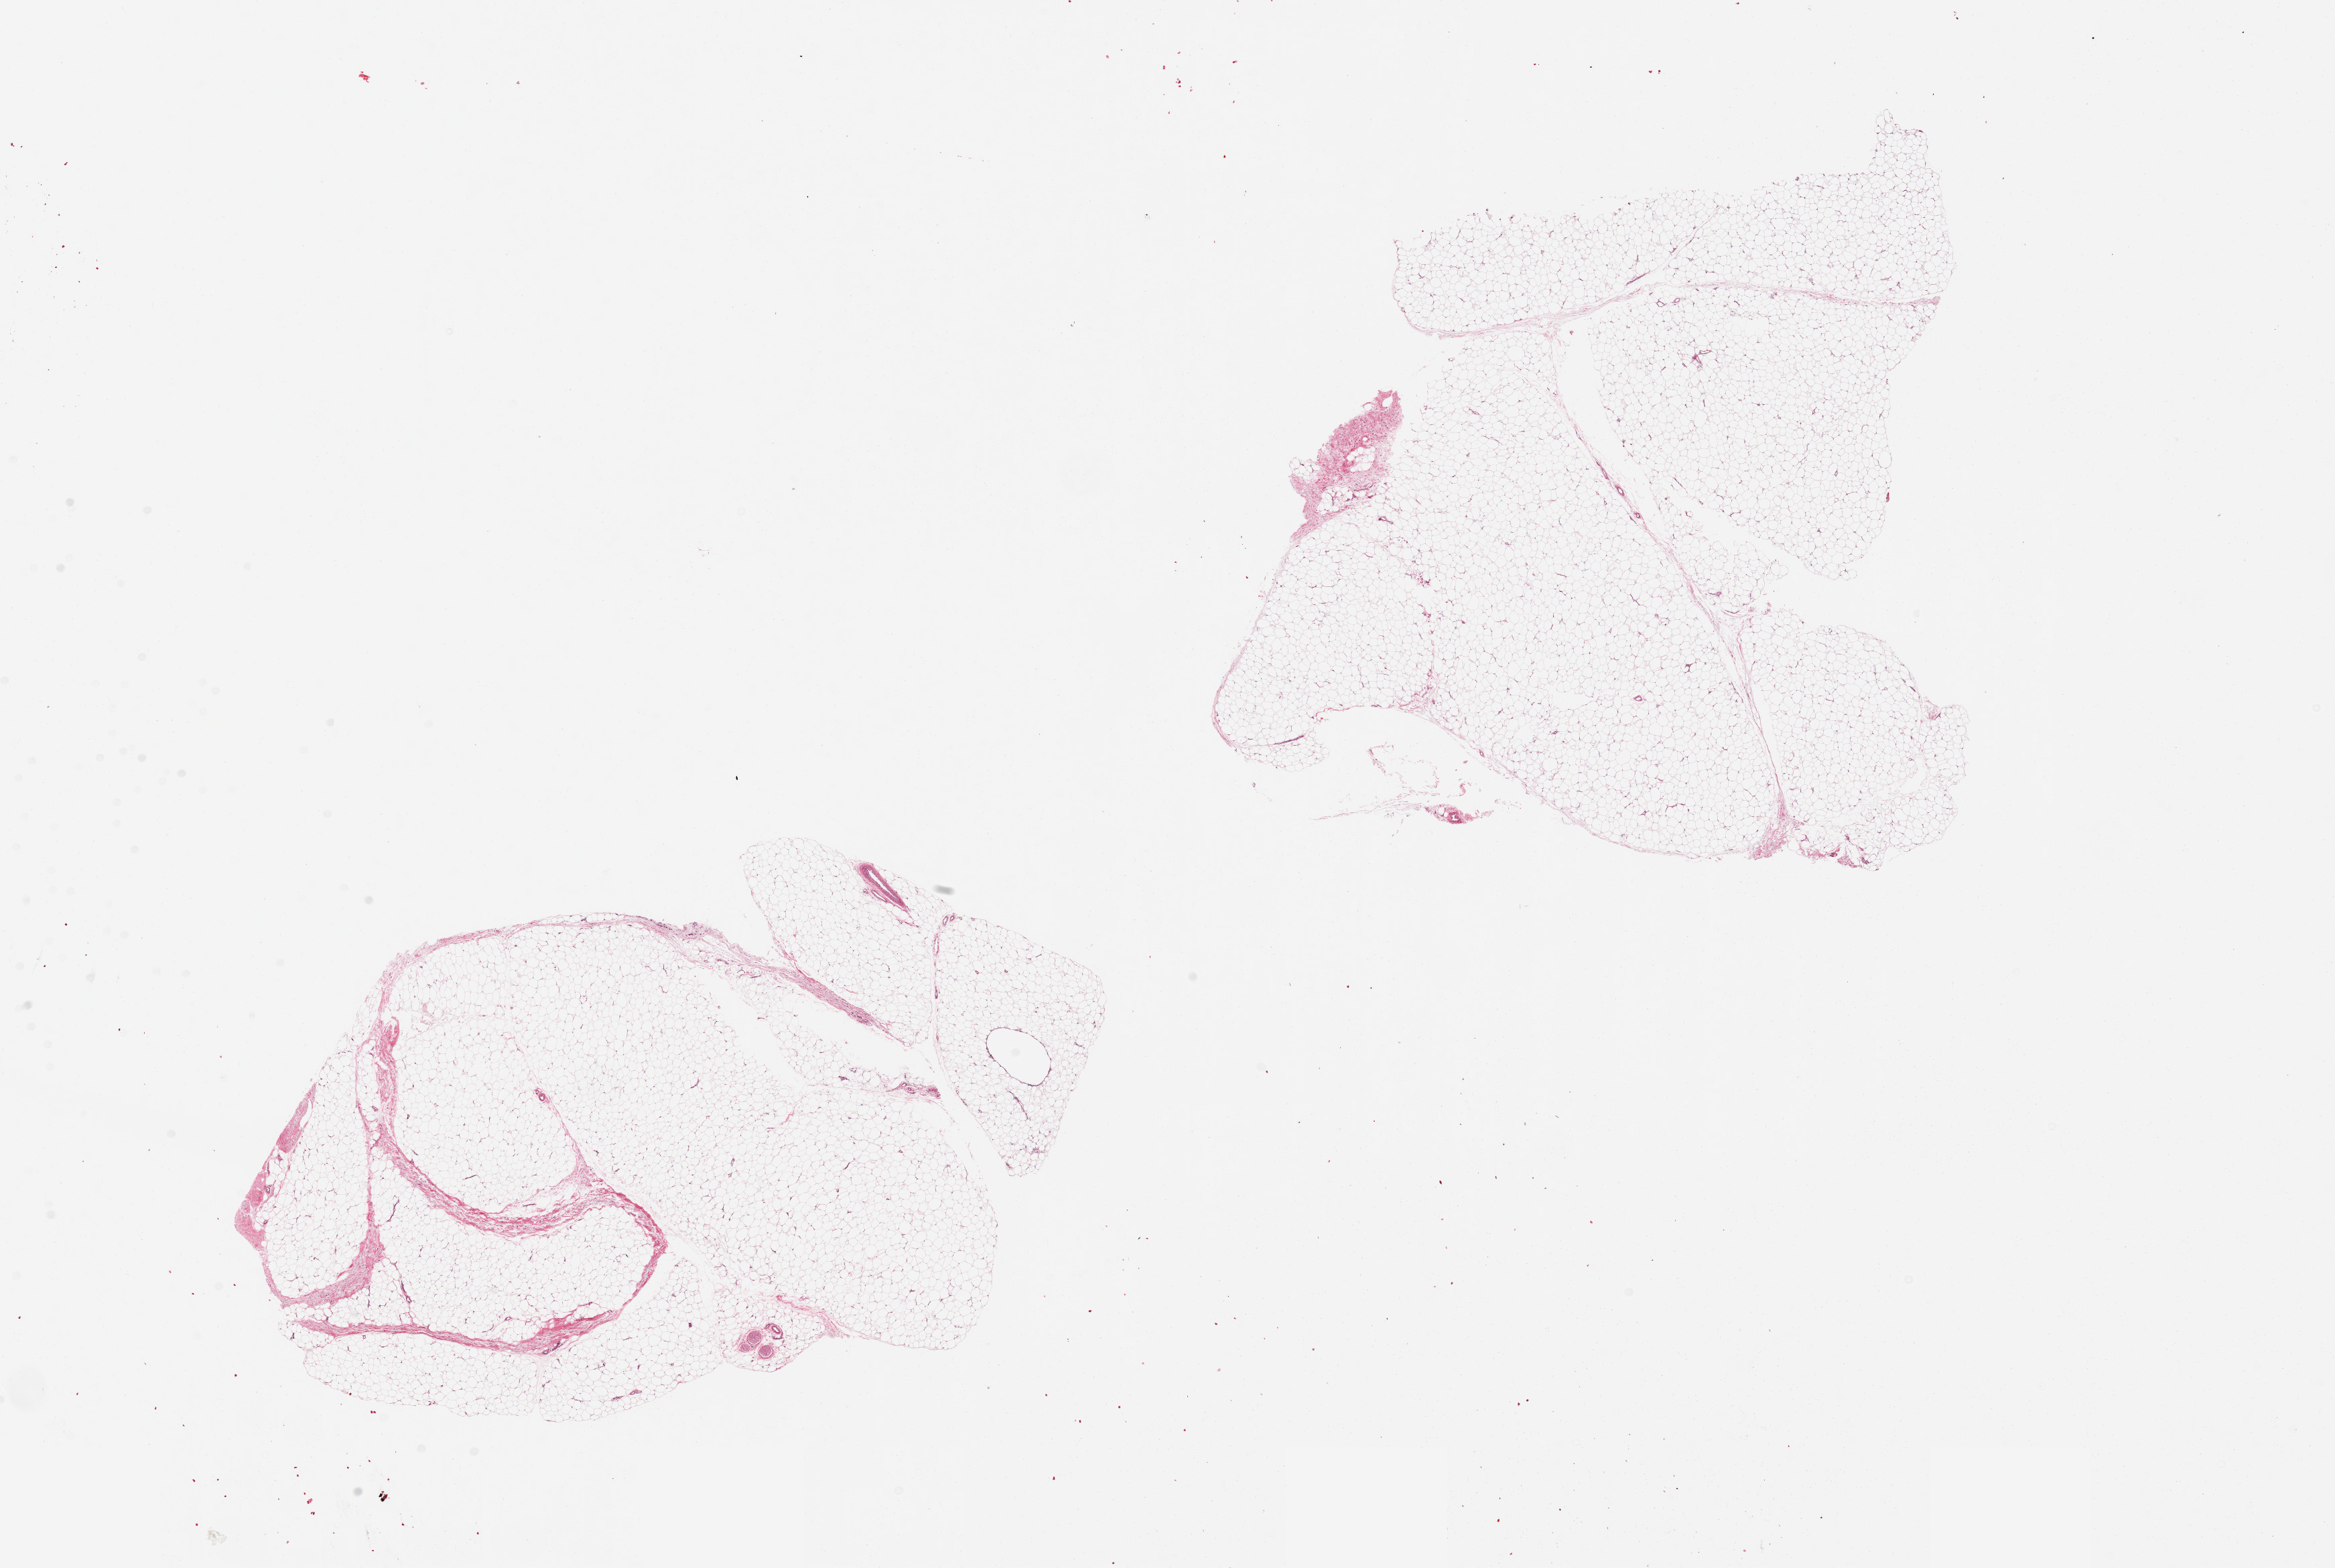
Whole-slide image, hematoxylin and eosin (H&E) stain, shown as a low-resolution overview of the whole scanned area (about 27.6 x 18.5 mm). PAXgene-fixed, paraffin-embedded tissue. Sampled site (target tissue): adipose tissue. Donor tissue sample. Female donor.
* review note (as recorded): 2 pieces, ~5-10% fascial tissue, rep delinated